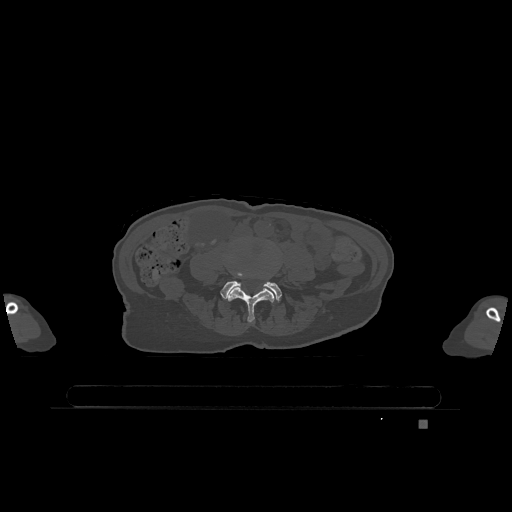
CT including the spine, one axial slice. Bone window (W 1800 / L 400 HU). 512 × 512 image matrix. Patient: female, 74 years. Case-level facts recorded for this patient, not image findings: primary cancer: lung; vertebrae with lytic lesions (as recorded): T1, T4, T5, T6, L4, L5.
Annotated regions visible in this slice (semi-automatically segmented with operator editing):
- L4 vertebra: bounding box <228,287,275,323> (left, top, right, bottom; pixels)
- L5 vertebra: <220,281,282,301>